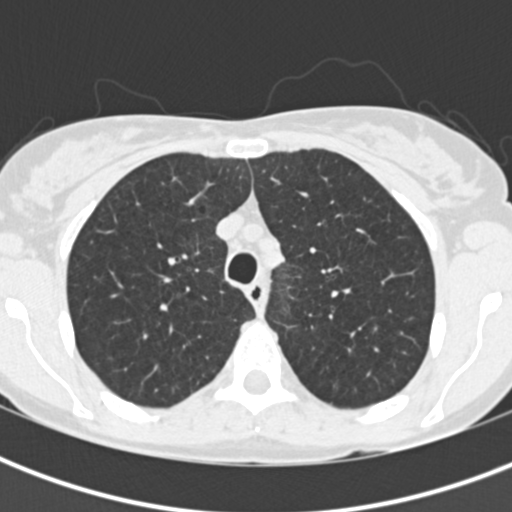
Axial slice from a low-dose chest CT screening exam, baseline screening round, lung window (W 1500 / L -600 HU), 2 mm slice thickness, standard (soft-tissue) reconstruction kernel (B30f), 512 × 512 image matrix. Female participant, aged 56 years at enrolment. Current smoker at enrolment.
Expert-annotated lung lesion, bounding box <357,305,402,350> (left, top, right, bottom; pixels). Reader record for this screening exam (exam-level; its link to the box is not recorded): non-calcified nodule or mass ≥4 mm, right upper lobe, 6 × 5 mm, poorly defined margins, ground glass attenuation. Note: the box lies in the patient's left hemithorax on this image, whereas the reader's record names the right lung; they may be different findings. Official screen result: positive, change unspecified: nodule(s) >= 4 mm or enlarging nodule(s), mass(es), or other non-specific abnormalities suspicious for lung cancer. Participant outcome: lung cancer diagnosed 124 days after this screen — small cell carcinoma, NOS, left lower lobe, stage IV (AJCC 6th edition), 80 mm at pathology.